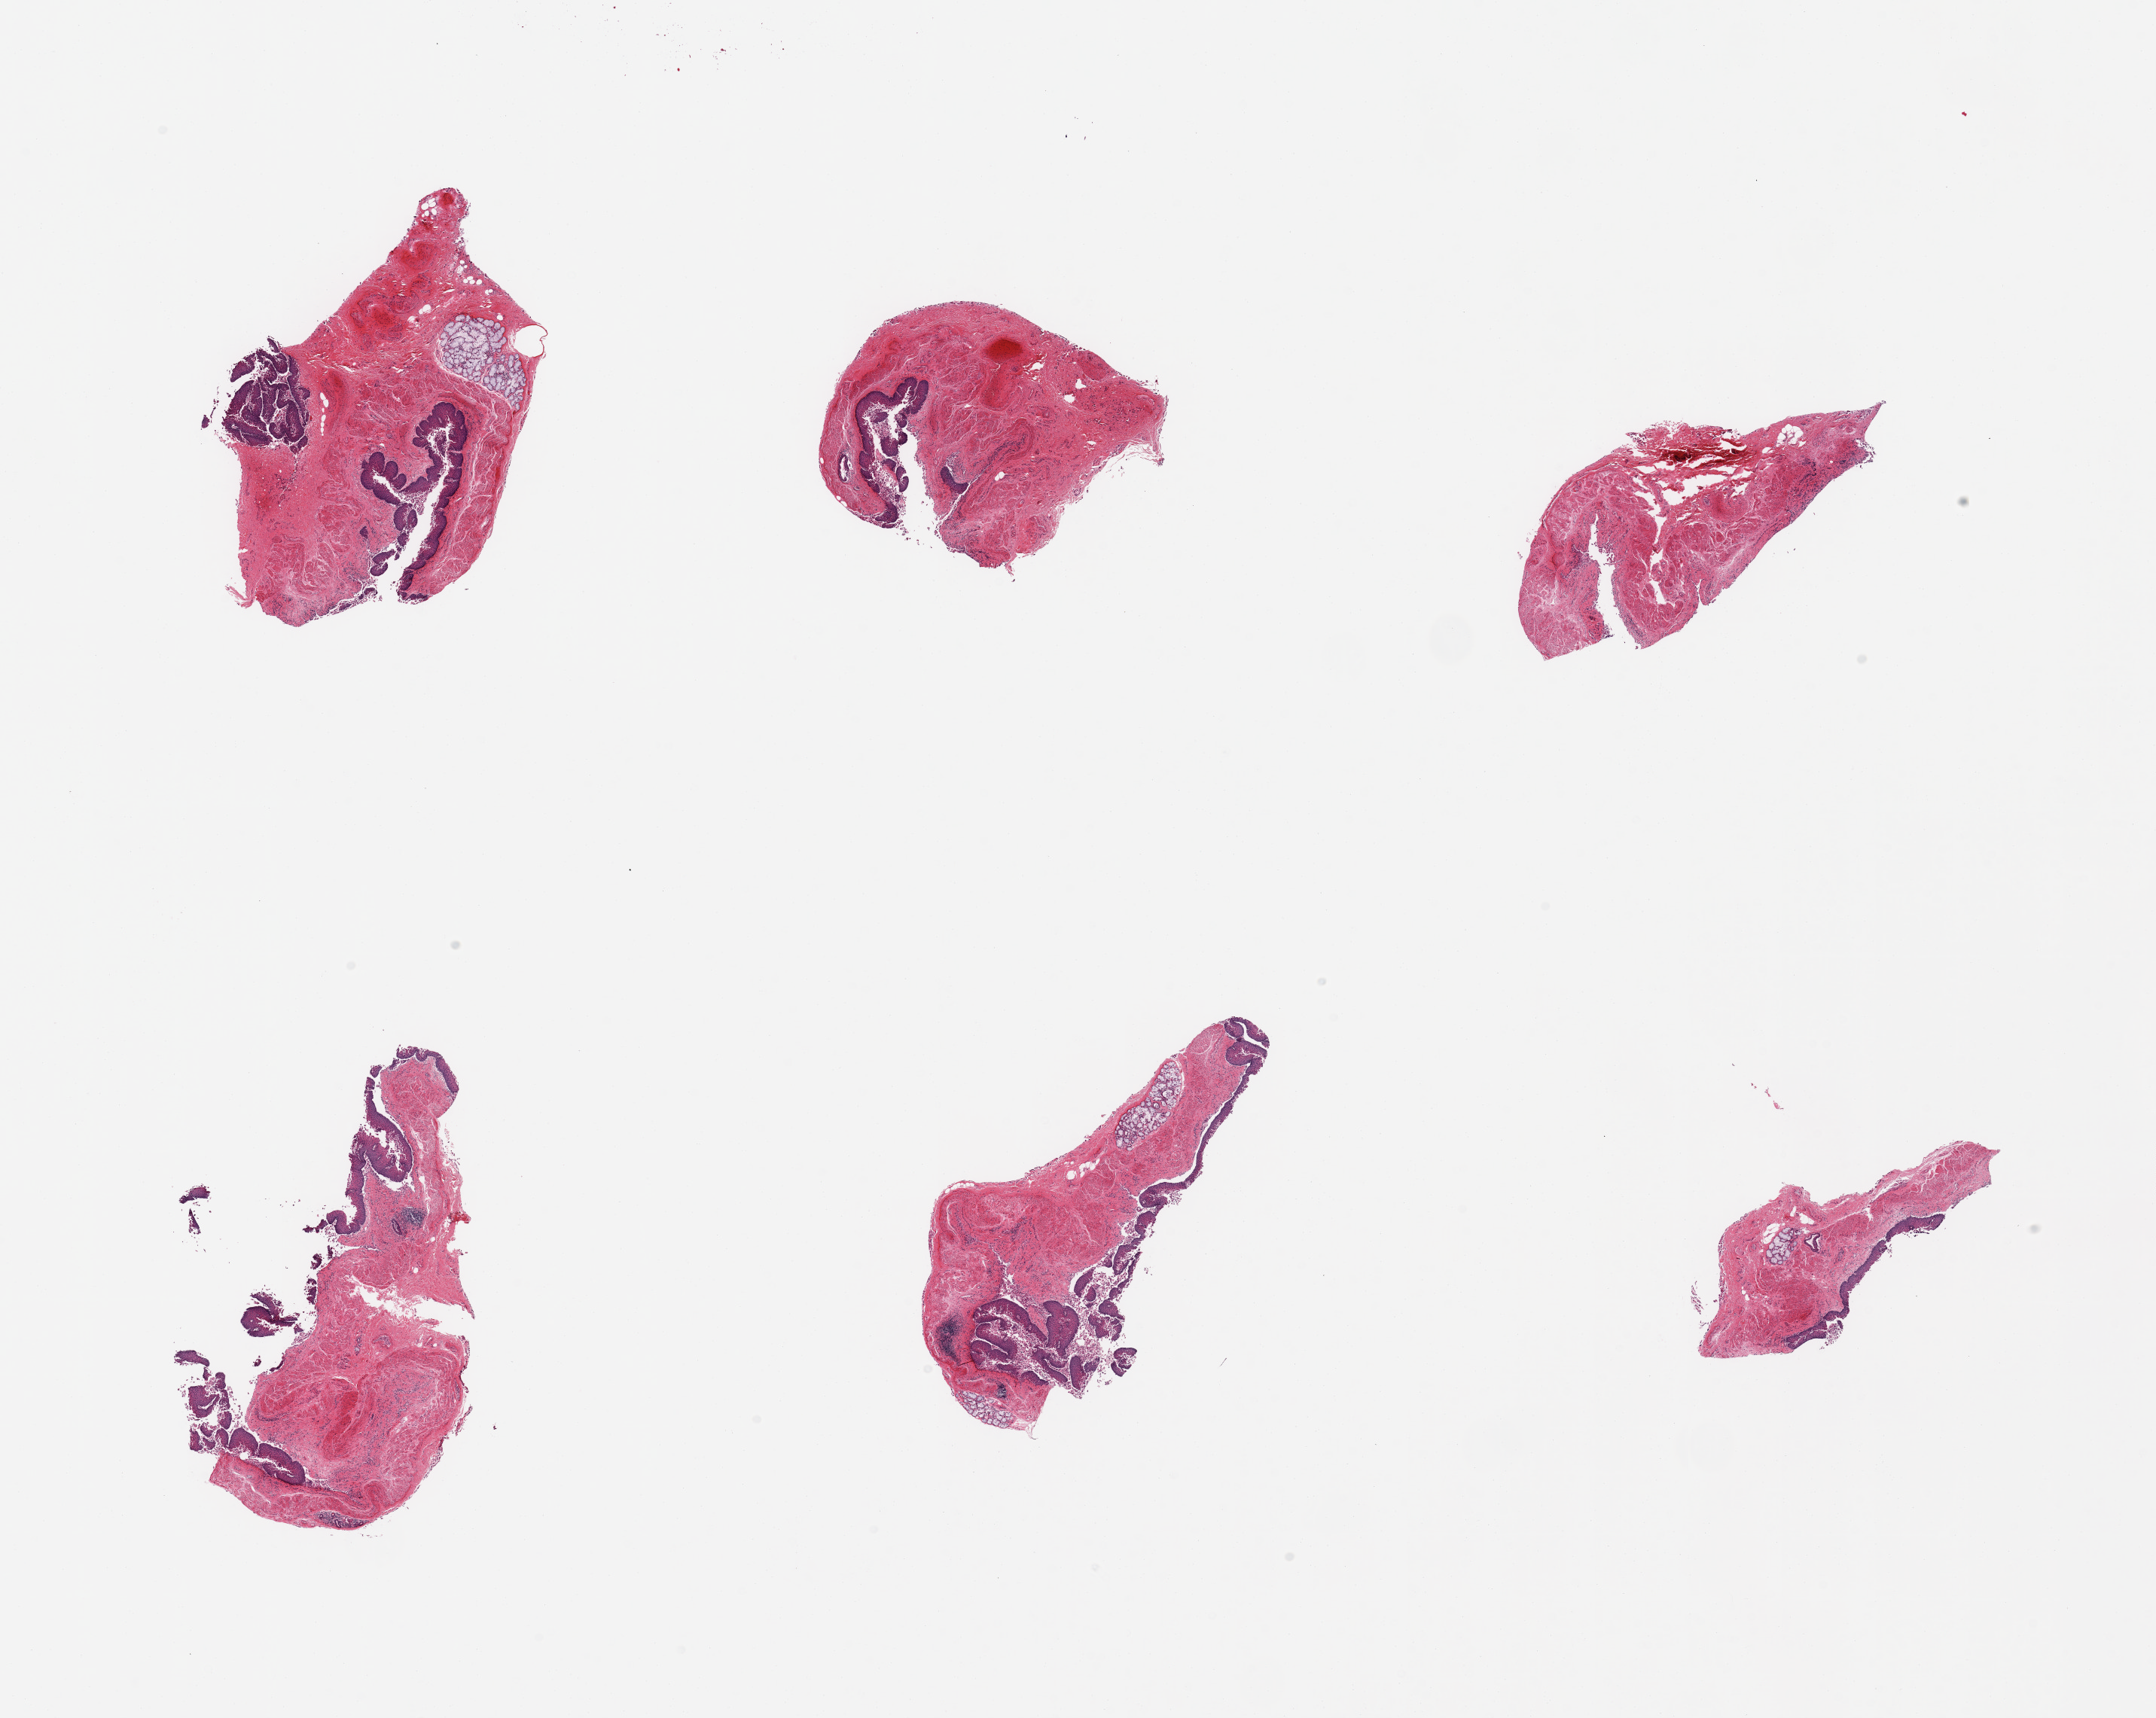
Digitized hematoxylin and eosin (H&E)-stained section, brightfield — shown as a low-resolution overview of the whole scanned area (about 22.6 x 18.0 mm, acquisition: 20x scan), PAXgene-fixed, paraffin-embedded tissue, sampled site (target tissue): esophageal mucous membrane, donor tissue sample. Male donor.
Reviewer comment on this tissue sample: 6 pieces; epithelium is partially sloughed, few clusters of submucosal glands.